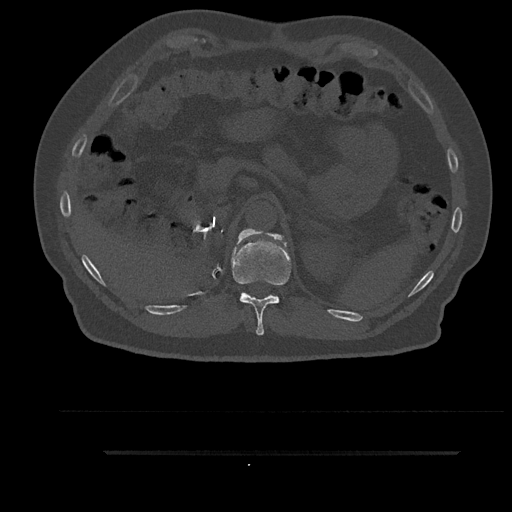
CT including the spine, one axial slice; reconstruction kernel Br40s/3; 120 kVp; bone window (W 1800 / L 400 HU); 0.5 mm slice thickness; 512 × 512 image matrix, field of view 432 × 432 mm. Patient: male, 63 years. Case-level facts recorded for this patient, not image findings: primary cancer: renal.
Structures marked on this image (semi-automatically segmented with operator editing):
- T11 vertebra: bounding box (x1, y1, x2, y2) in pixels: (231, 229, 291, 335)
- T12 vertebra: (237, 229, 258, 243)